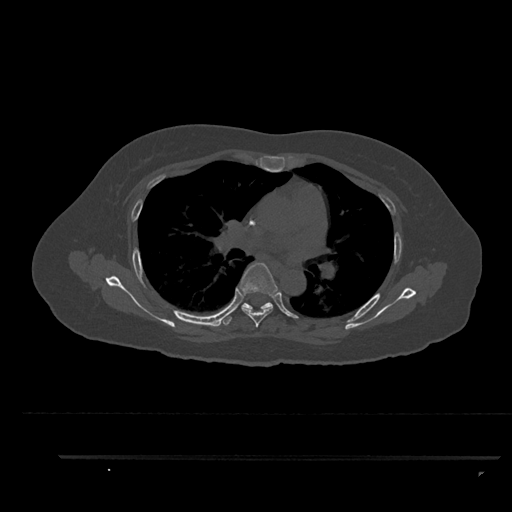
CT including the spine, one axial slice. Reconstruction kernel Br40s/3. Bone window (W 1800 / L 400 HU). 512 × 512 image matrix, field of view 408 × 408 mm. Female patient, age 44 years. Case-level facts recorded for this patient, not image findings: primary cancer: renal; vertebrae with lytic lesions (as recorded): L1.
Annotated regions visible in this slice (semi-automatically segmented with operator editing):
- T5 vertebra: bounding box (x1, y1, x2, y2) in pixels: (239, 262, 278, 328)
- T6 vertebra: (224, 302, 273, 325)